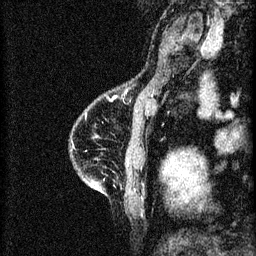
Breast MRI (dynamic contrast-enhanced), one sagittal slice; 3 images stored at this slice position (order not interpretable as contrast timing); 1.5 T; TE 4.2 ms, TR 8.2 ms; 2 mm slice thickness; 256 × 256 image matrix. Female patient, age 46 years.
Structures marked on this image (semi-automatic segmentation, software-assisted and operator-edited):
- analysis volume of interest (the breast-tissue region the enhancement analysis was run in; not a lesion): bounding box <71,114,148,209> (left, top, right, bottom; pixels)
- tumour enhancement mask (voxels above the 70 % enhancement threshold inside the analysis volume of interest): <92,182,95,185>